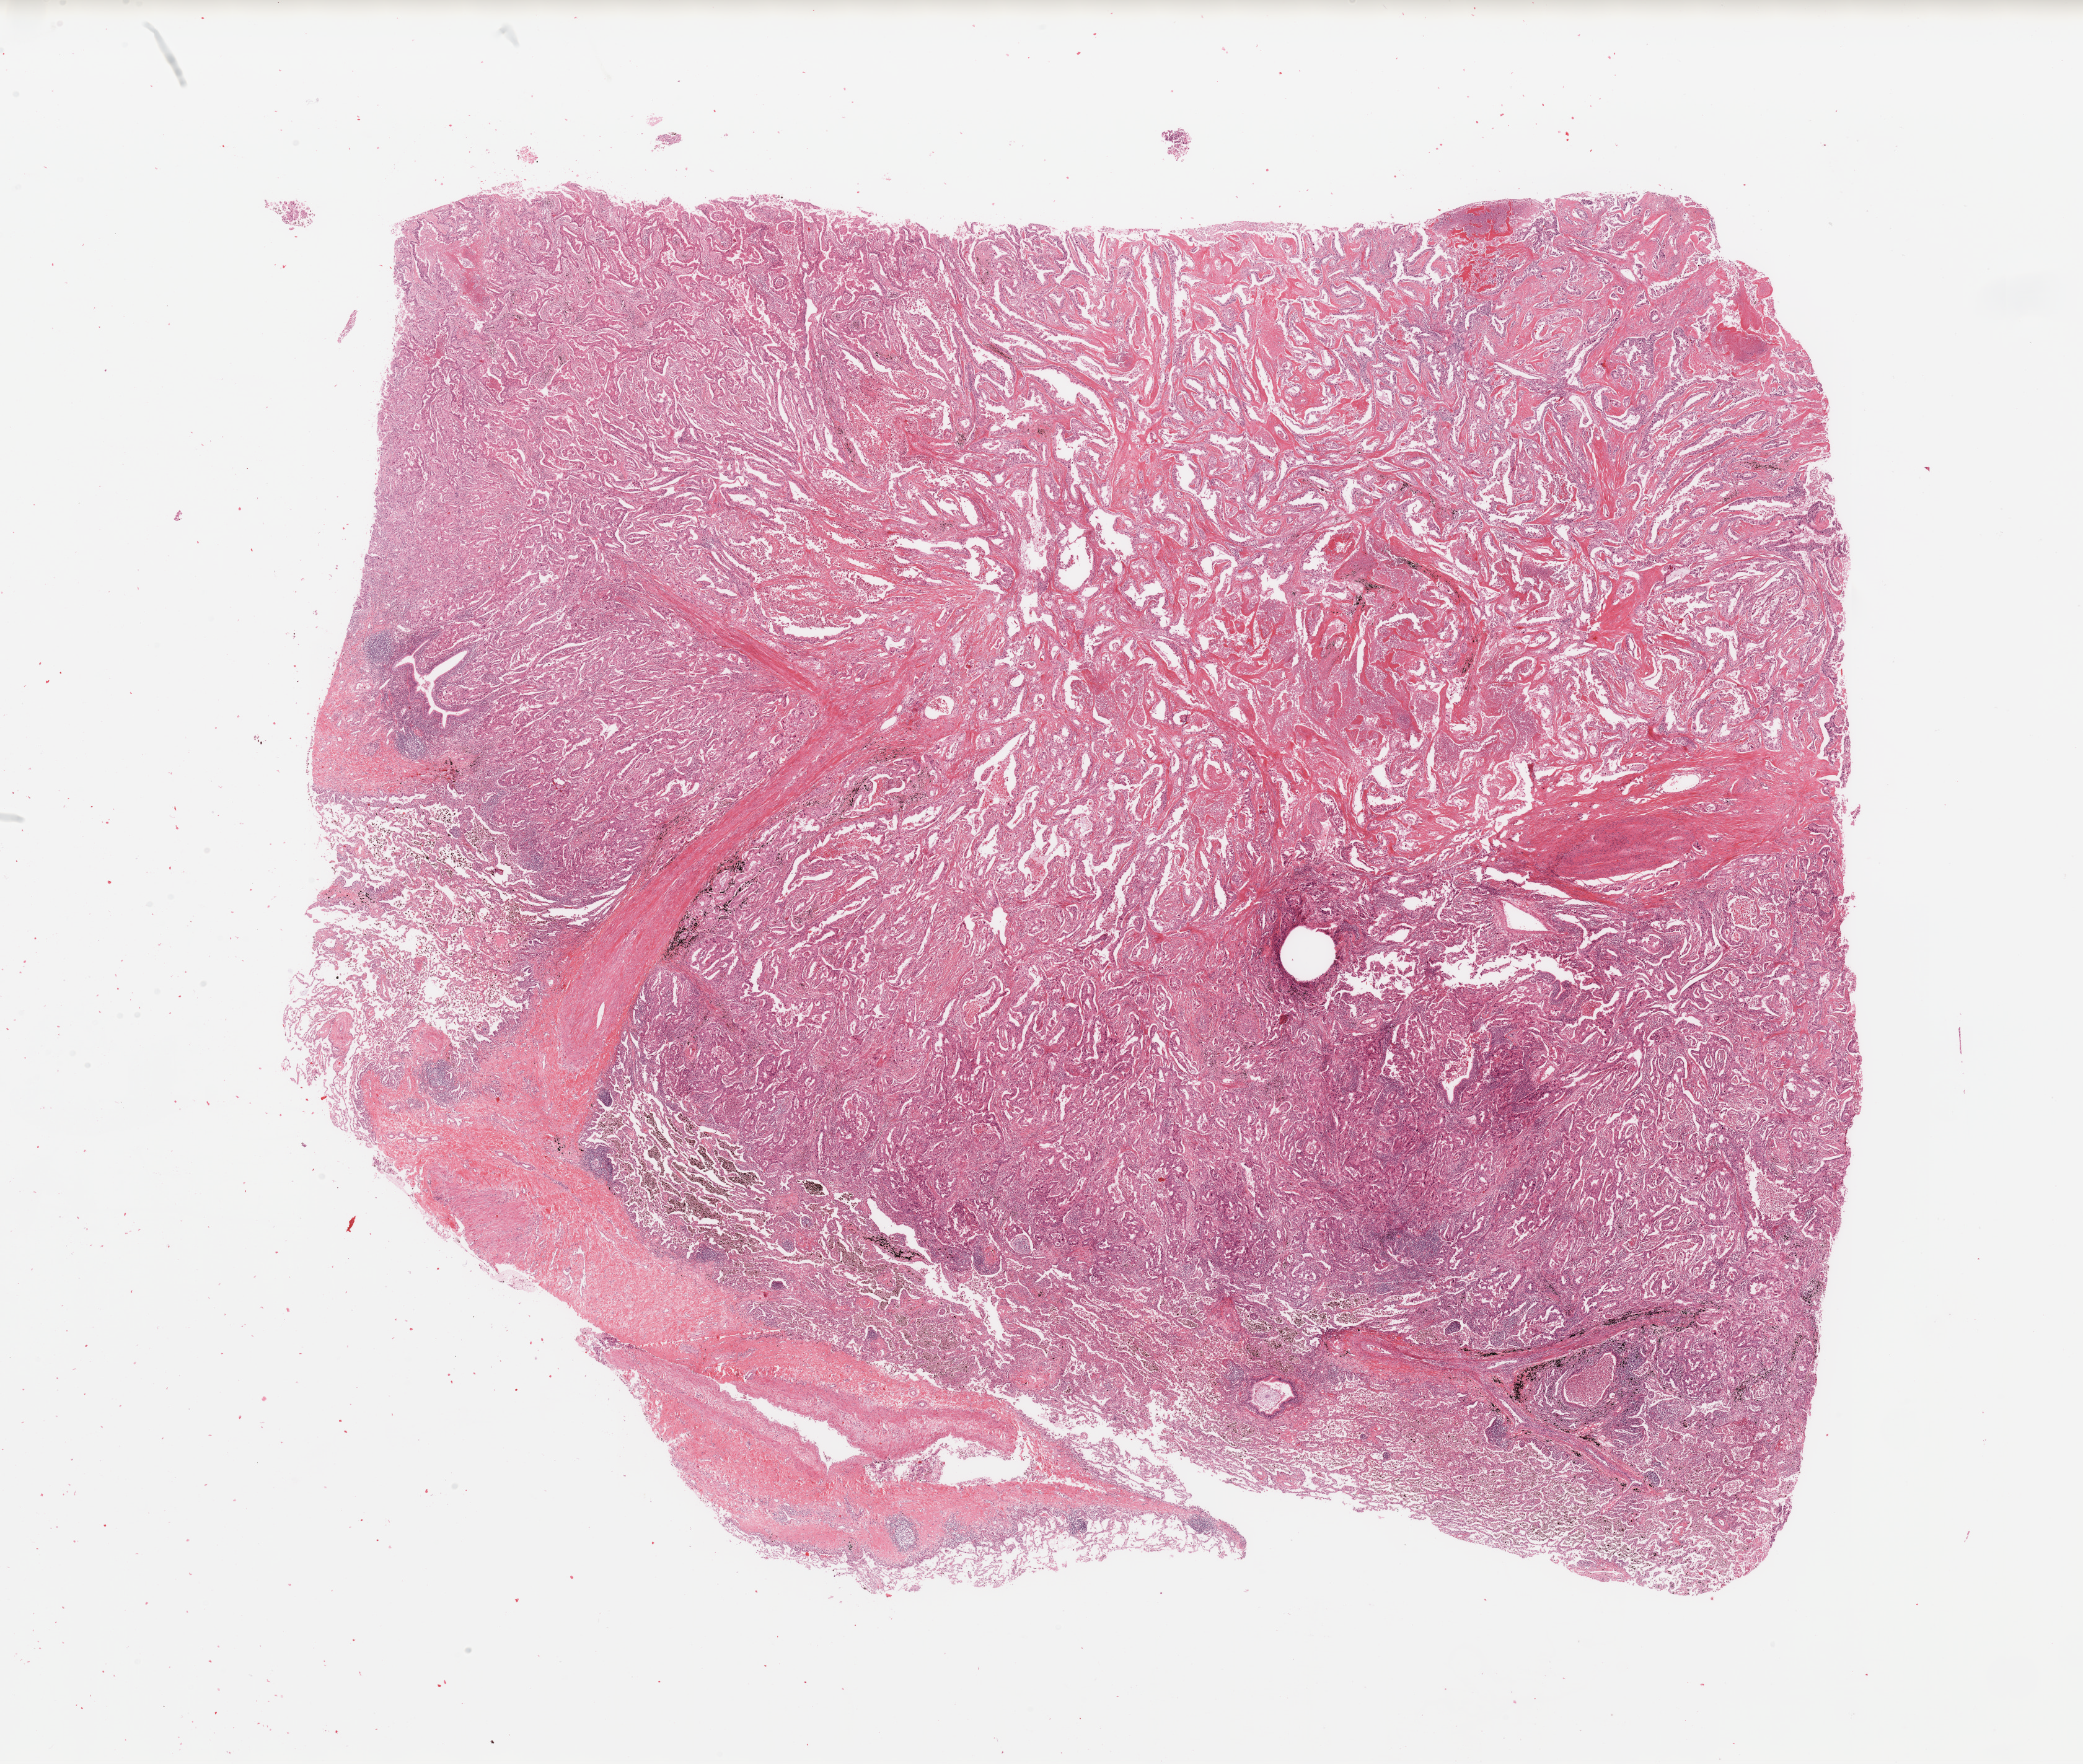
Whole-slide histology image, H&E — low-resolution overview of the scanned area, about 26.6 x 22.5 mm (from a 20x scan), tumour tissue sample, sampled site: lung. Patient: male, age 64 years. Histologic grade: G2 (moderately differentiated). Pathologist review of this section (percent, as recorded): tumour nuclei 75%, necrosis 2%.
• AJCC pathologic stage: IIB
• histologic diagnosis: Adenocarcinoma, NOS